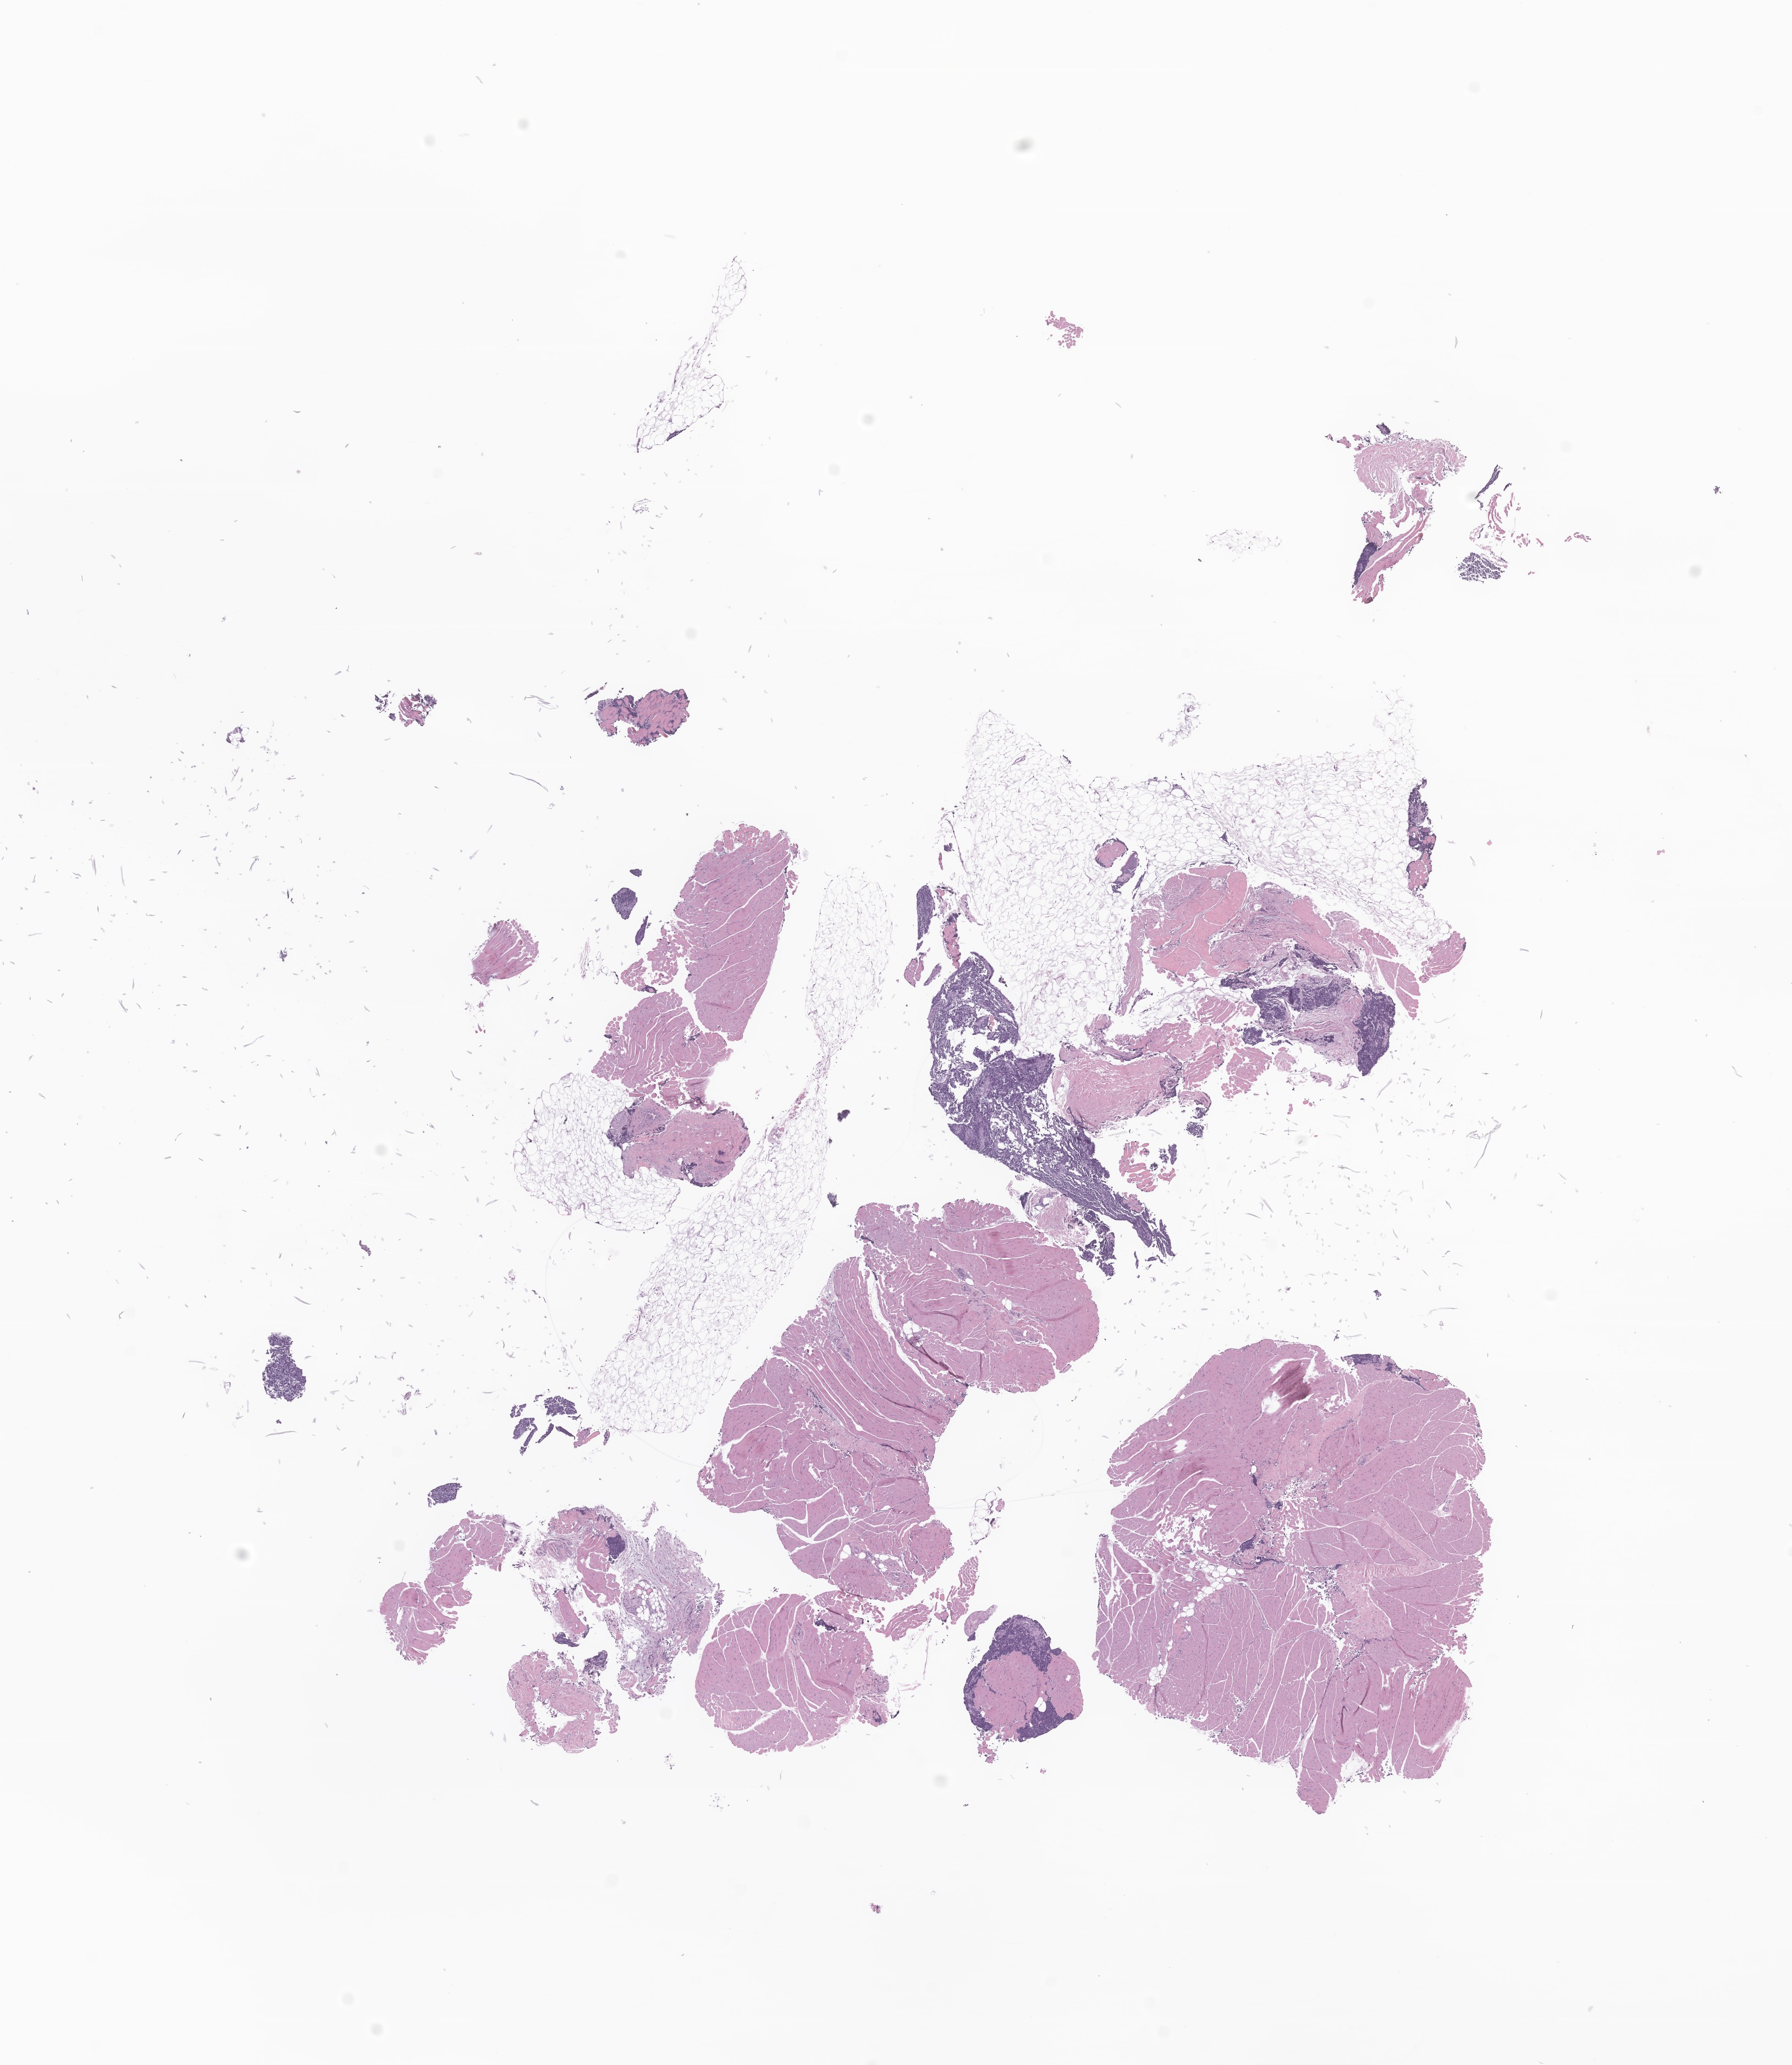
Haematoxylin and eosin whole-slide image of tumor tissue from the soft tissue of lower extremity — a low-resolution overview of the entire scanned area, about 13.7 x 15.8 mm, FFPE section. Patient male; age 937 days.
Diagnosis: Alveolar rhabdomyosarcoma.